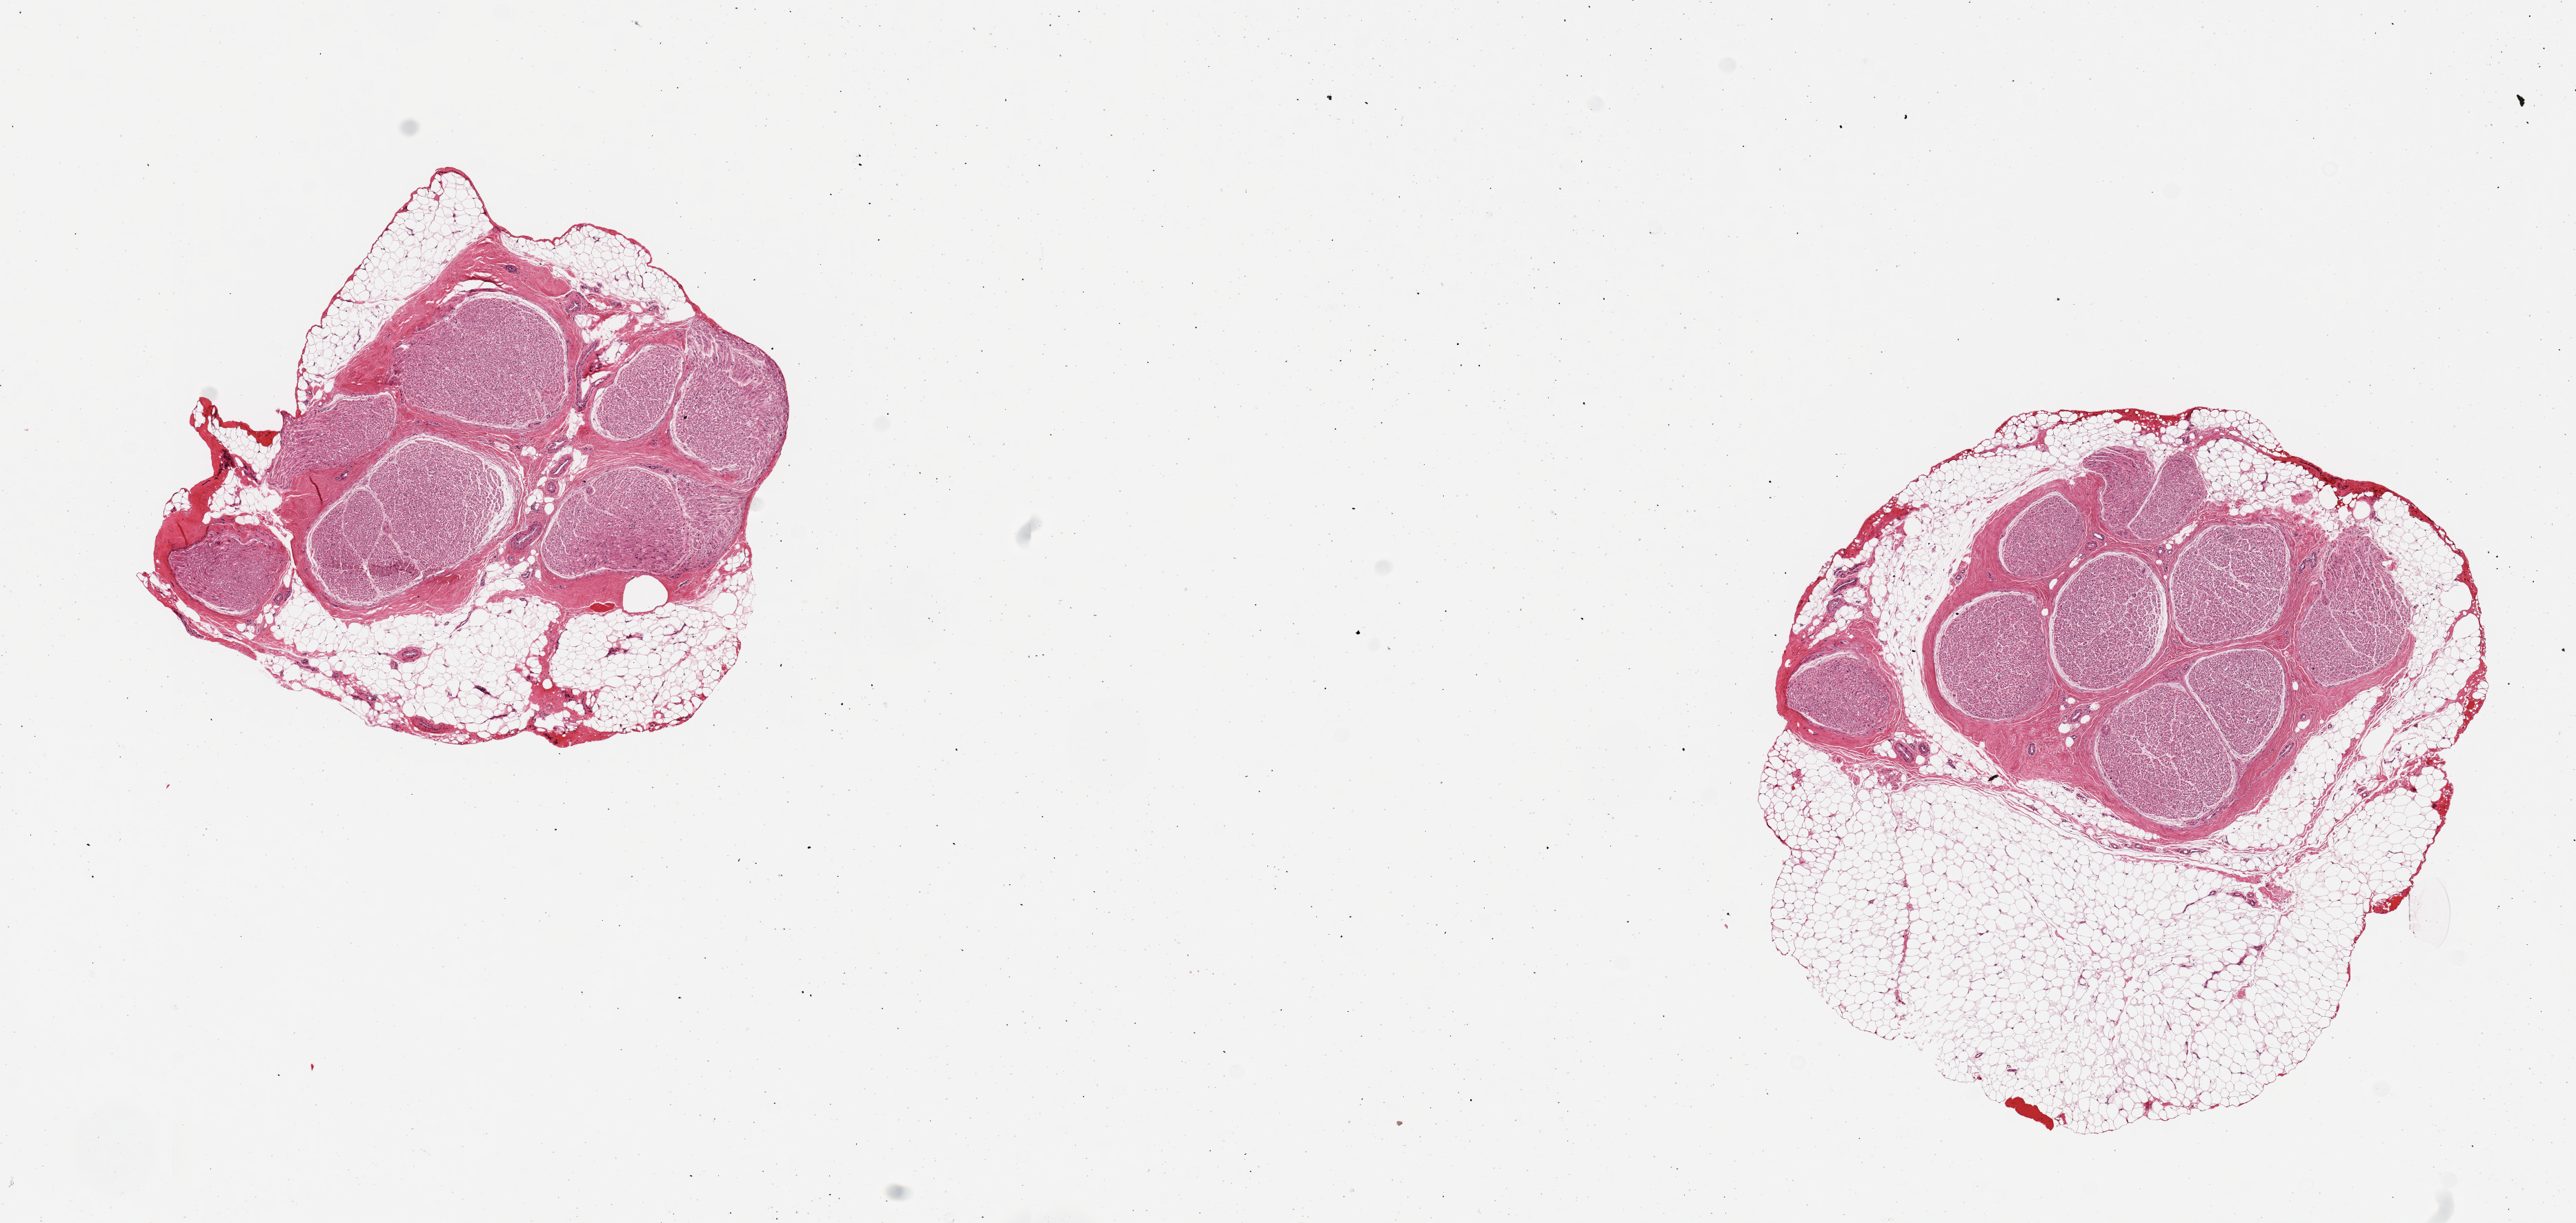
Hematoxylin and eosin (H&E) whole-slide image, a low-resolution overview of the entire scanned area, about 14.8 x 7.0 mm, PAXgene-fixed, paraffin-embedded tissue, target tissue: tibial nerve, donor tissue sample. Donor: female.
Reviewer comment on this tissue sample: 2 pieces, extensive adherent fat, rims of up to ~1.5mm.